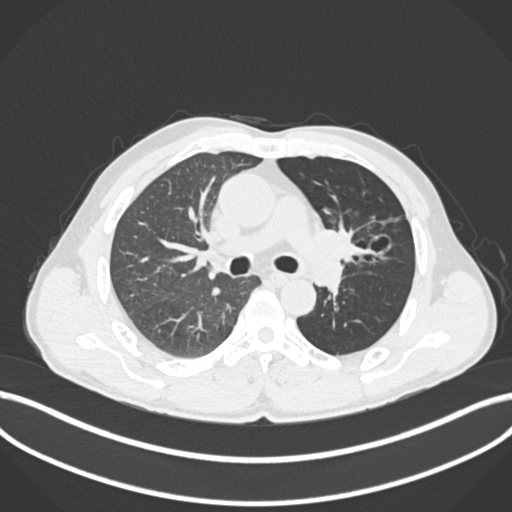
Chest CT, one axial slice. Slice 117 of 255 in the series (ordered by position). Reconstruction kernel B30f. 120 kVp. Lung window (W 1500 / L -600 HU). 1 mm slice thickness. 512 × 512 image matrix, field of view 400 × 400 mm. Patient: male, 57 years. From the clinical record (not read from this slice): clinical TNM (as recorded): T2b N0 M0.
Structures marked on this image (bounding box drawn by a radiologist):
- lung tumour (recorded histology: squamous cell carcinoma): bounding box [x1, y1, x2, y2] px = [313, 221, 376, 267]